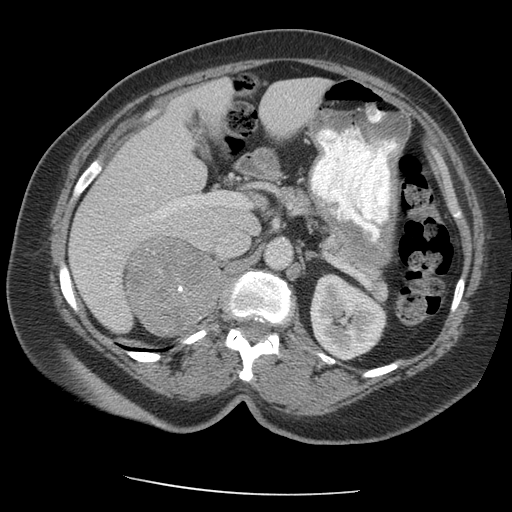
Contrast-enhanced abdominal CT, one axial slice; position 123 of 163 along the scan axis; 140 kVp; intravenous contrast given; soft-tissue window (W 400 / L 40 HU); 2.5 mm slice thickness; 512 × 512 image matrix. Female patient, age 70 years. From the clinical record (not read from this slice): diagnosis: adrenocortical carcinoma; tumour side: right adrenal; tumour size at pathology: 9.5 cm; Ki-67 index: 5 %; stage (as recorded): 2.
Annotated regions visible in this slice (semi-automatic segmentation, software-assisted and operator-edited):
- mass: bounding box (x1, y1, x2, y2) in pixels: (128, 239, 219, 336)